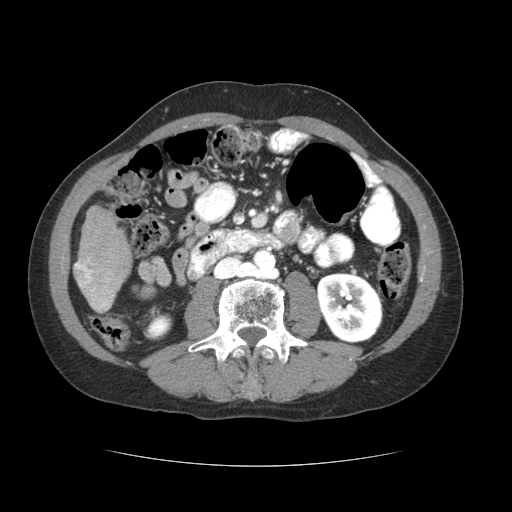
Contrast-enhanced abdominal CT (liver protocol), one axial slice. Position 12 of 69 along the scan axis. Soft-tissue window (W 400 / L 40 HU). 512 × 512 image matrix, field of view 360 × 360 mm. From the clinical record (not read from this slice): diagnosis: hepatocellular carcinoma (patient treated with transarterial chemoembolisation; whether this scan precedes or follows treatment is not stated here); TNM stage (as recorded): Stage-II; Child-Pugh class: B; tumour differentiation: poorly differentiated; tumour nodularity: multinodular.
Annotated regions visible in this slice (semi-automatically segmented with operator editing):
- liver parenchyma outside the tumour (the mass and vessels are separate outlines, so this box may not span the whole liver): bounding box [x1, y1, x2, y2] px = [74, 206, 132, 312]
- liver vessels: [75, 259, 113, 310]